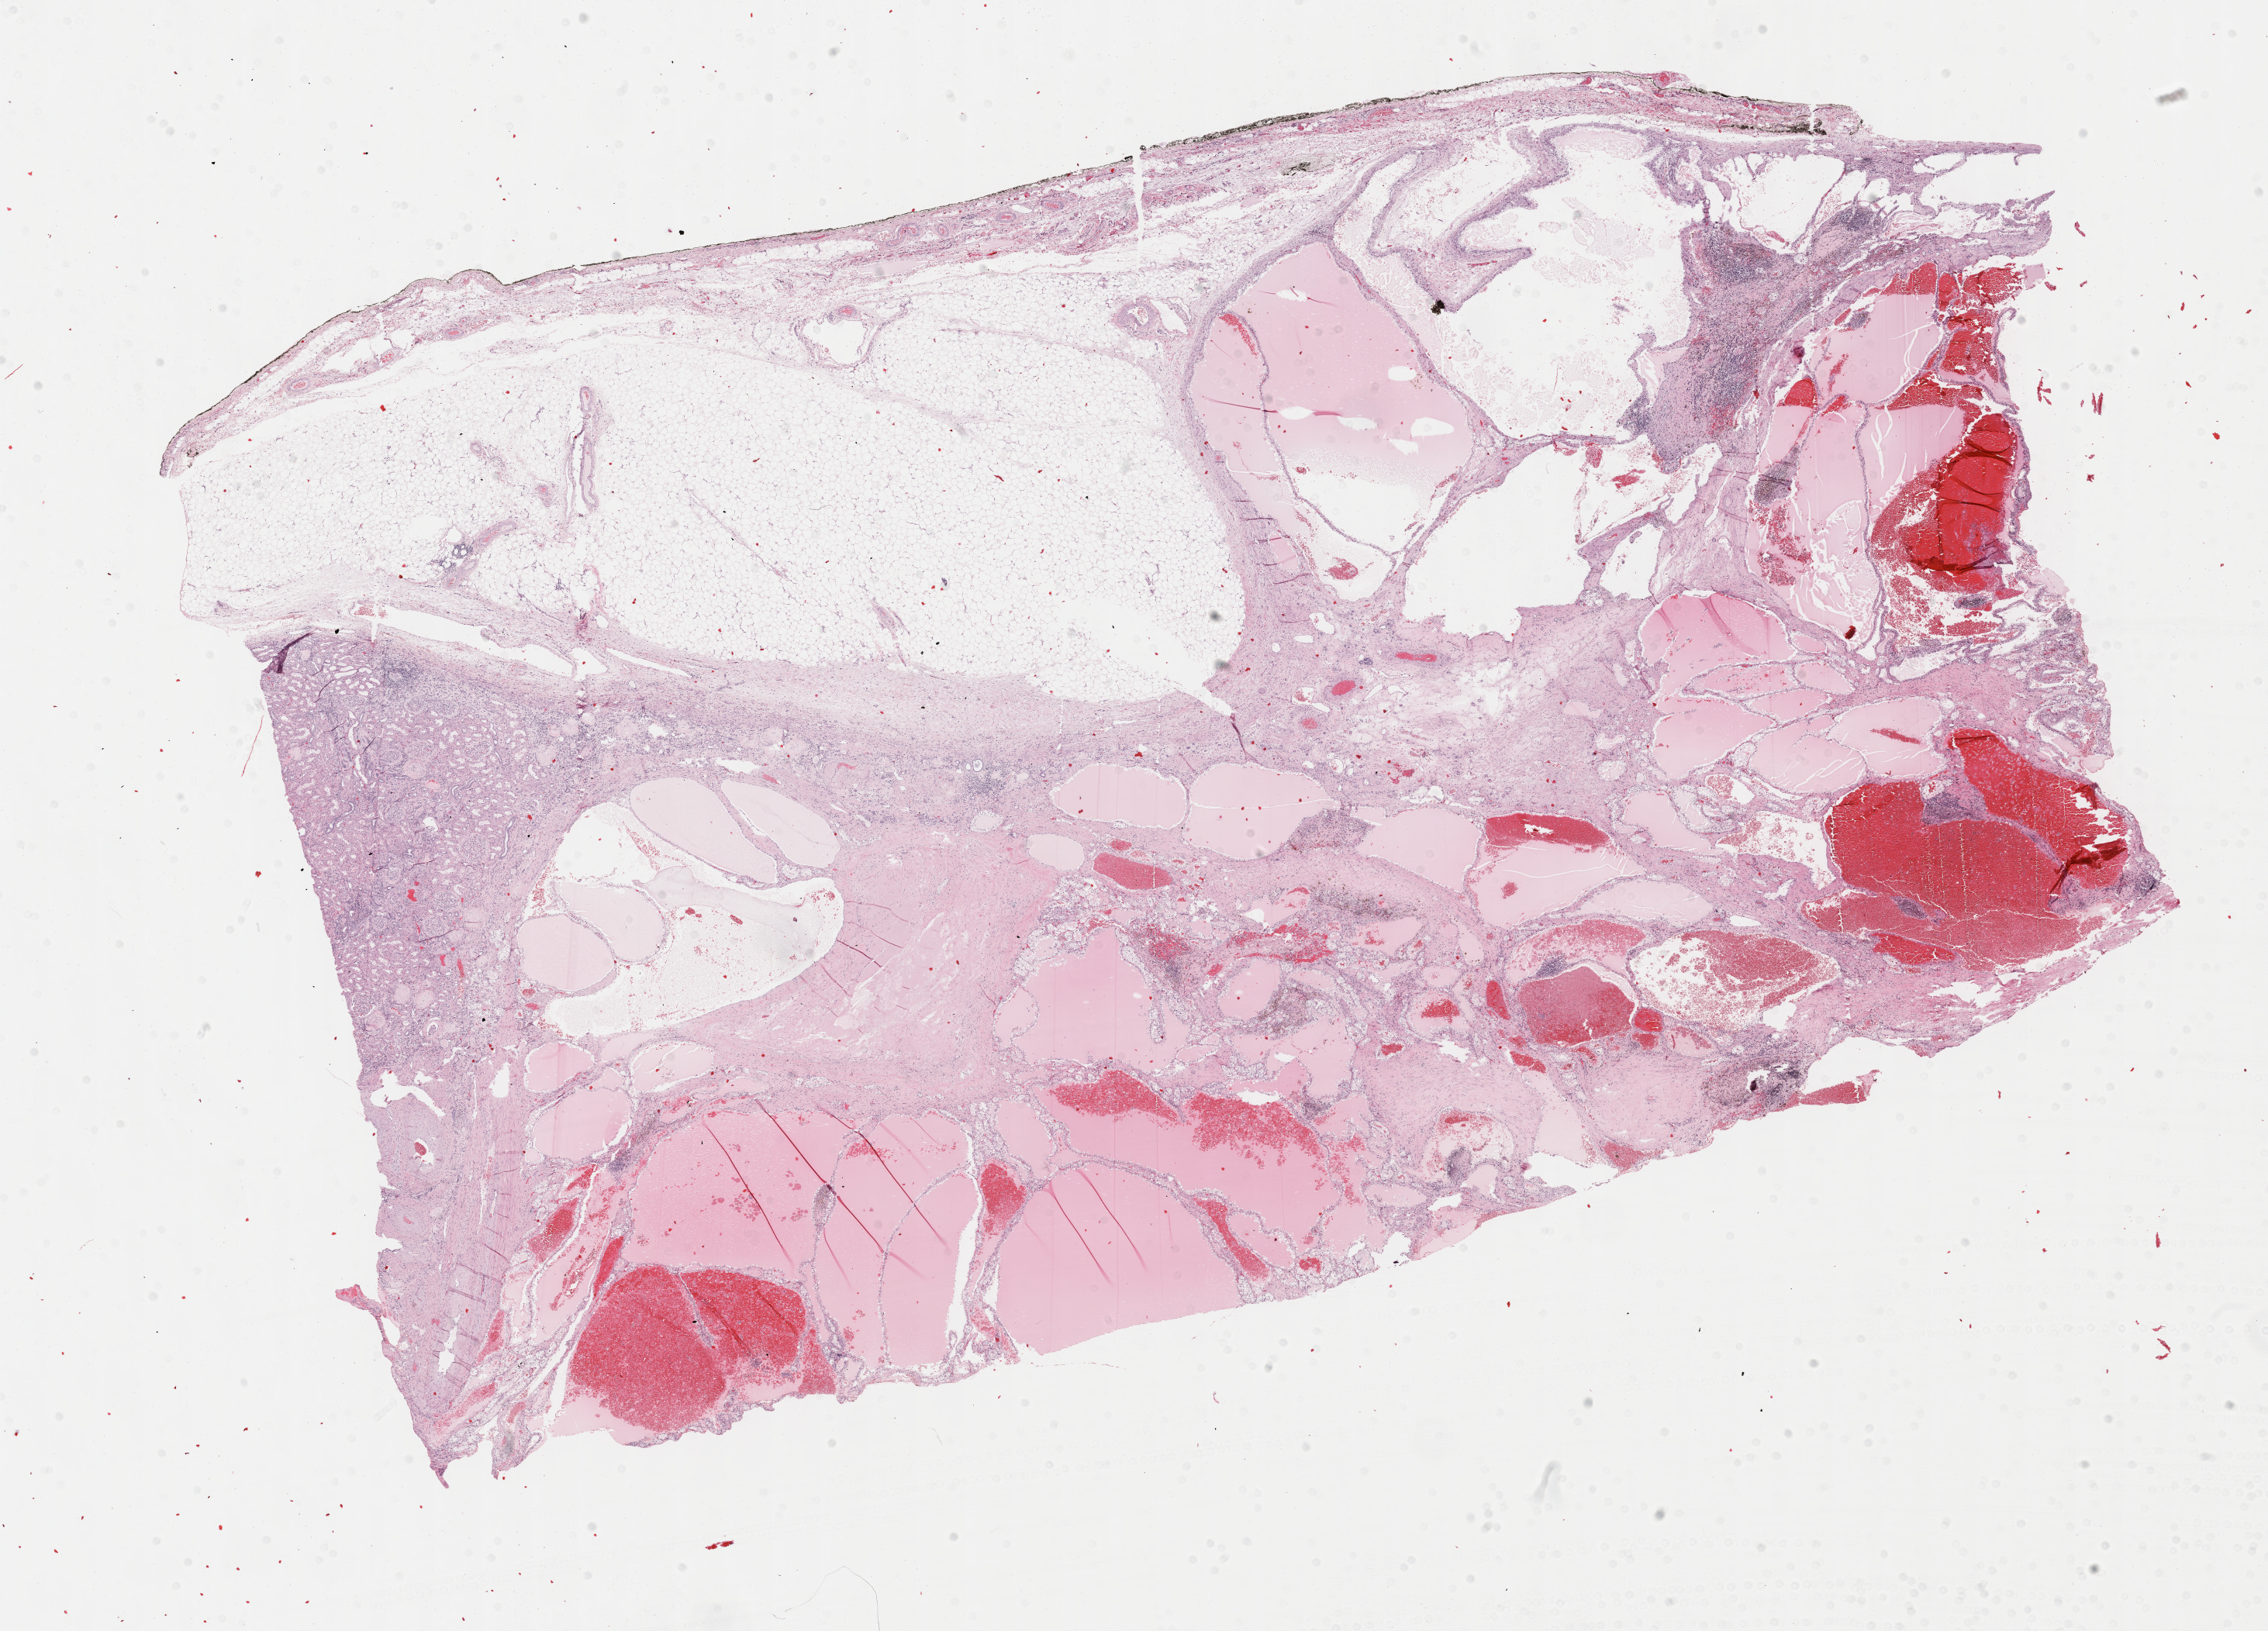
H&E whole-slide image, whole scanned area (about 23.7 x 17.0 mm) shown as a low-resolution overview, formalin-fixed paraffin-embedded (FFPE) diagnostic section, sample: primary tumour, bladder. Male, age 46 years at initial diagnosis. Histologic grade: high grade.
* AJCC pathologic stage: III
* lymph nodes positive (case pathology): 0 of 21 examined
* diagnosis: Papillary transitional cell carcinoma